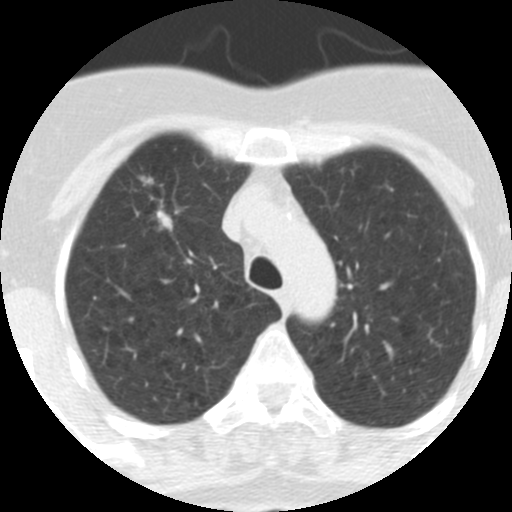
Chest CT (low-dose screening protocol), one axial image, first (baseline) screen, lung window (W 1500 / L -600 HU), 2.5 mm slice thickness, 120 kVp, 512 × 512 image matrix, field of view 253 × 253 mm. Female, age 62 years at enrolment. Current smoker at enrolment.
Lesion marked by an expert reader, bounding box (x1, y1, x2, y2) in pixels: (116, 164, 185, 234). The exam's reader record, not a measurement of the box and not confirmed to be the same lesion: non-calcified nodule or mass ≥4 mm, right upper lobe, 9 × 7 mm, spiculated (stellate) margins, soft tissue attenuation. Lung cancer was diagnosed 126 days after this screen: adenocarcinoma, NOS, right upper lobe, moderately differentiated (G2), stage IA (AJCC 6th edition), 18 mm at pathology.